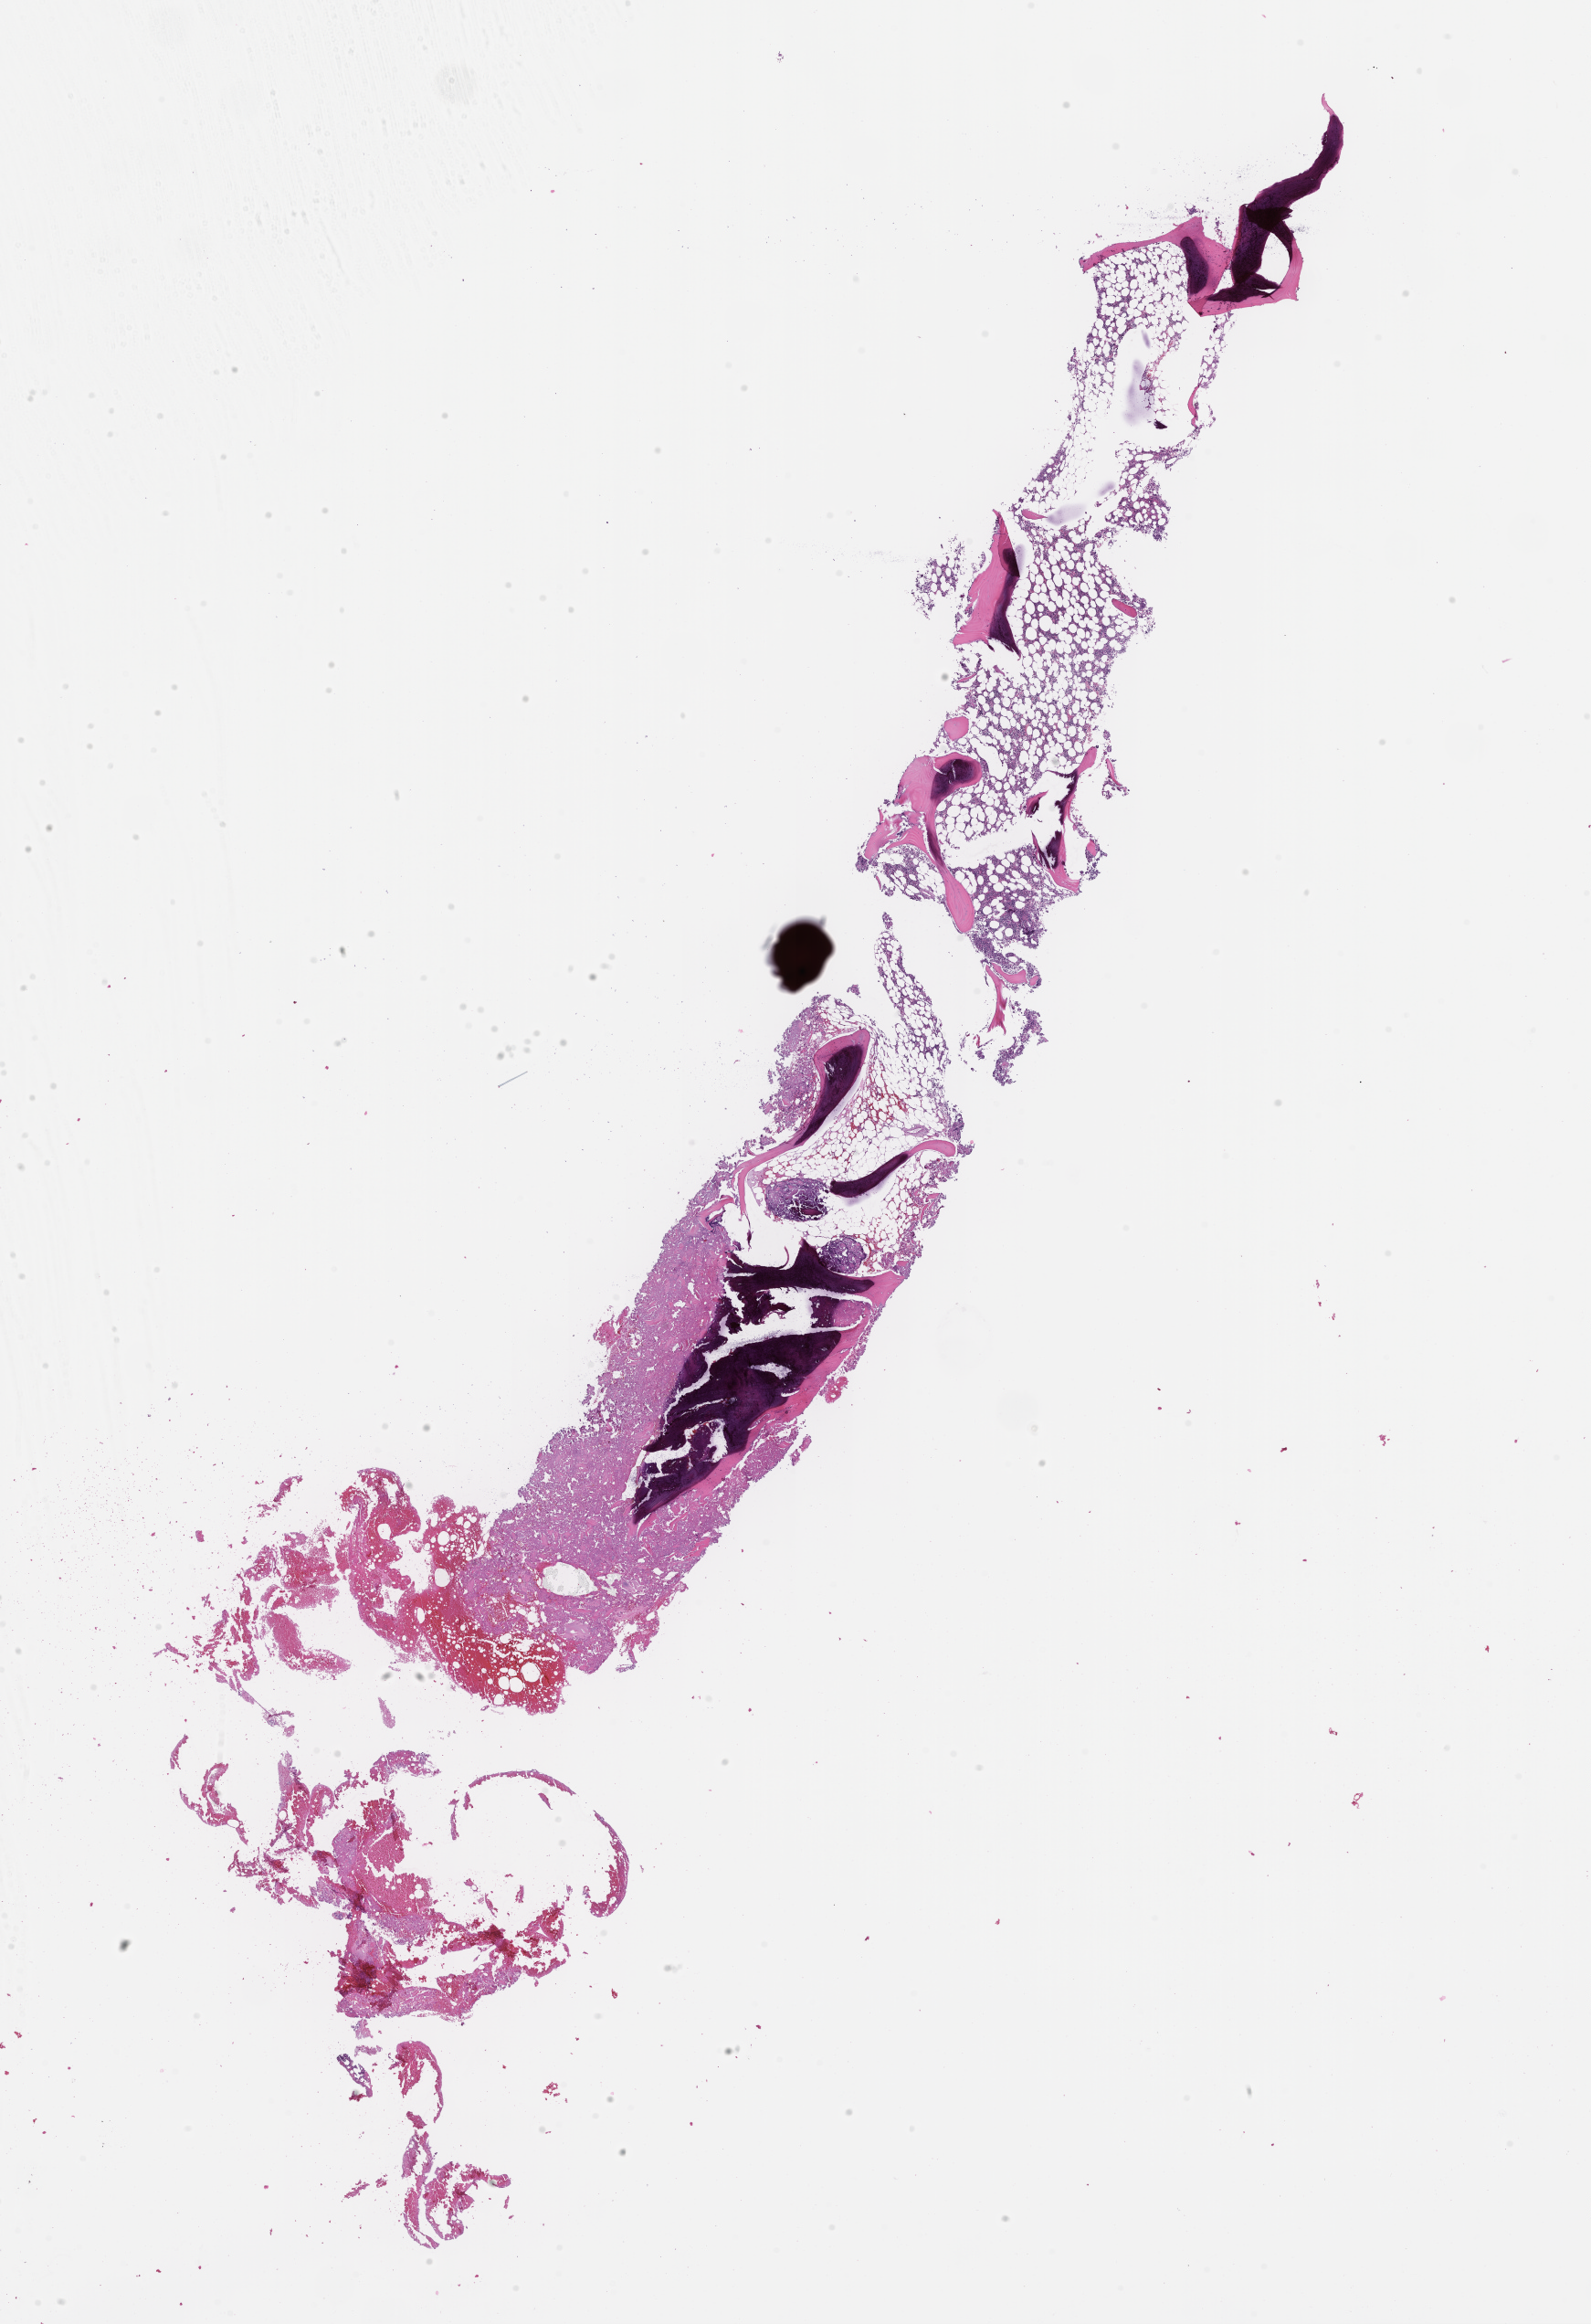
Hematoxylin and eosin (H&E) whole-slide image, whole scanned area (about 14.1 x 20.6 mm) shown as a low-resolution overview, formalin-fixed paraffin-embedded section, tissue site: bone marrow. Patient: male.
This section: primary tumour tissue. Diagnosis: Plasma Cell Myeloma.